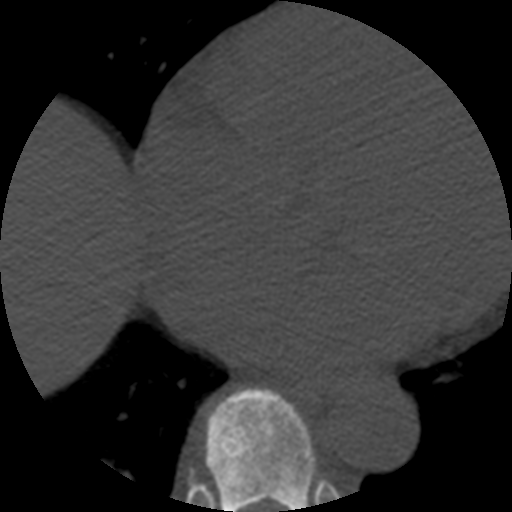
CT including the spine, one axial slice; position 318 of 508 along the scan axis; 120 kVp; bone window (W 1800 / L 400 HU); 512 × 512 image matrix, field of view 160 × 160 mm. Patient age 57 years. From the clinical record (not read from this slice): primary cancer: prostate.
Annotated regions visible in this slice (semi-automatically segmented with operator editing):
- T8 vertebra: bounding box [x1, y1, x2, y2] px = [206, 389, 317, 512]